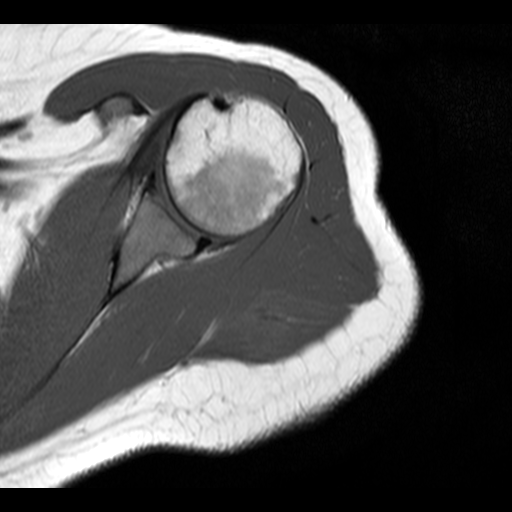
MRI of an extremity soft-tissue mass, one axial slice; slice 13 of 20 in the series (ordered by position); 512 × 512 image matrix, field of view 150 × 150 mm. Female patient. From the clinical record (not read from this slice): histological type: malignant fibrous histiocytoma; grade: low; site of the primary tumour: left arm.
Structures marked on this image (expert manual segmentation):
- gross tumour volume (mass): box from (x=237, y=292) to (x=286, y=326) px